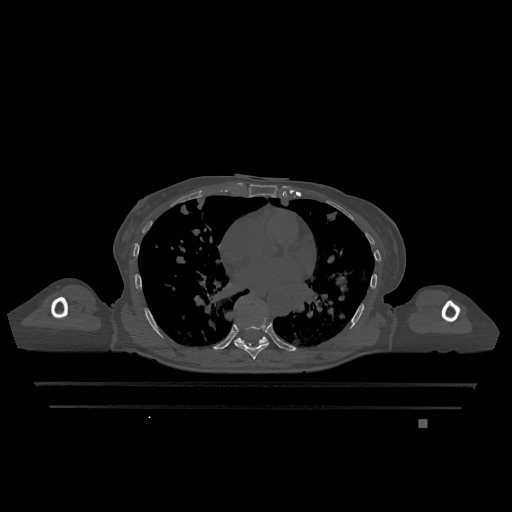
CT including the spine, one axial slice. Position 722 of 1317 along the scan axis. Bone window (W 1800 / L 400 HU). 0.5 mm slice thickness. 512 × 512 image matrix, field of view 500 × 500 mm. Female patient, age 74 years. From the clinical record (not read from this slice): primary cancer: lung; vertebrae with lytic lesions (as recorded): T1, T4, T5, T6, L4, L5.
Structures marked on this image (semi-automatically segmented with operator editing):
- T7 vertebra: bounding box <235,316,269,360> (left, top, right, bottom; pixels)
- T9 vertebra: <234,302,268,345>